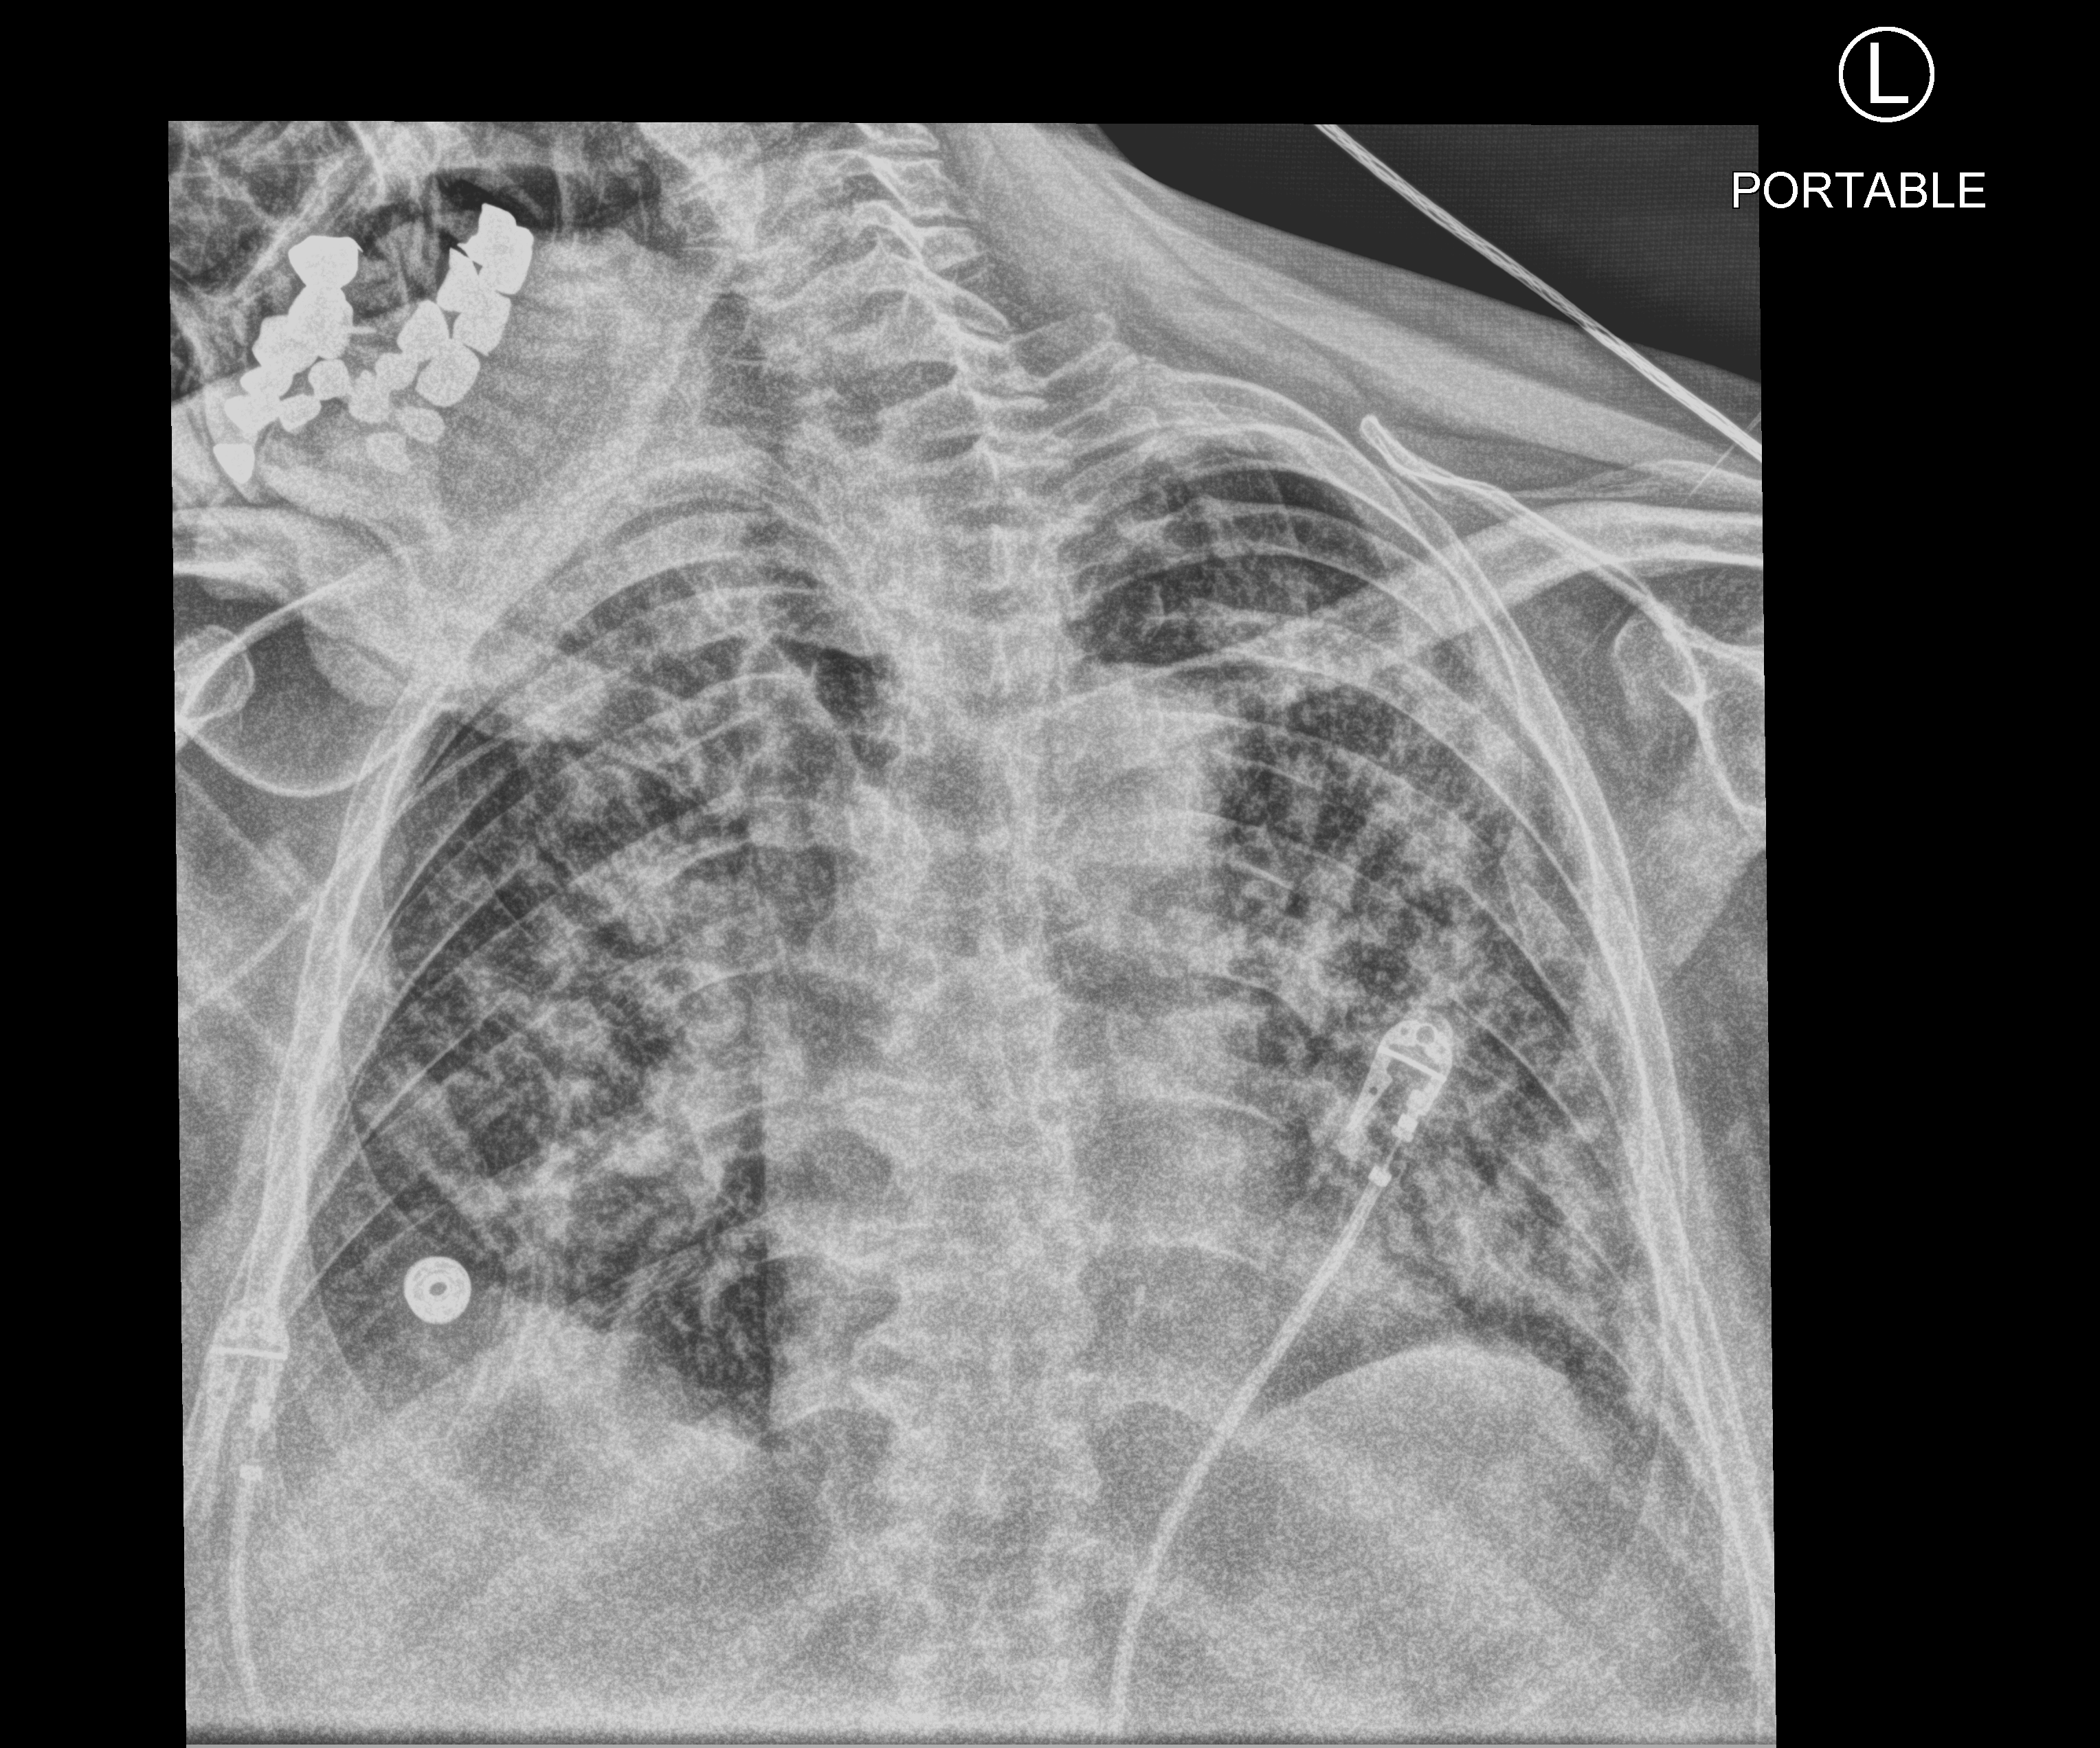
Chest X-ray (portable); anteroposterior (AP) projection. Male patient hospitalised with COVID-19, age 60–74 years.
Hospital-stay facts (about this admission, not read from this image; timing relative to this image not recorded): chronic kidney disease (admission record): no; admitted to intensive care during this hospital stay: yes; length of hospital stay: 24 days.